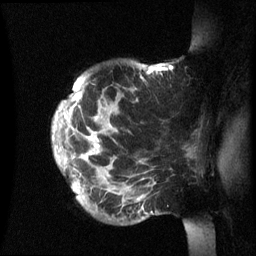
Breast MRI (dynamic contrast-enhanced), one sagittal slice. Slice 49 of 60 in the series (ordered by position). Dynamic contrast-enhanced series, image 2 of 3 at this slice position (ordered by acquisition). 1.5 T. TE 4.2 ms, TR 8.4 ms. 2.4 mm slice thickness. 256 × 256 image matrix, field of view 230 × 230 mm. Female patient, age 48 years.
Structures marked on this image (semi-automatic segmentation, software-assisted and operator-edited):
- analysis volume of interest (the breast-tissue region the enhancement analysis was run in; not a lesion): box from (x=52, y=63) to (x=202, y=236) px
- tumour enhancement mask (voxels above the 70 % enhancement threshold inside the analysis volume of interest): (x=53, y=67)–(x=163, y=192)